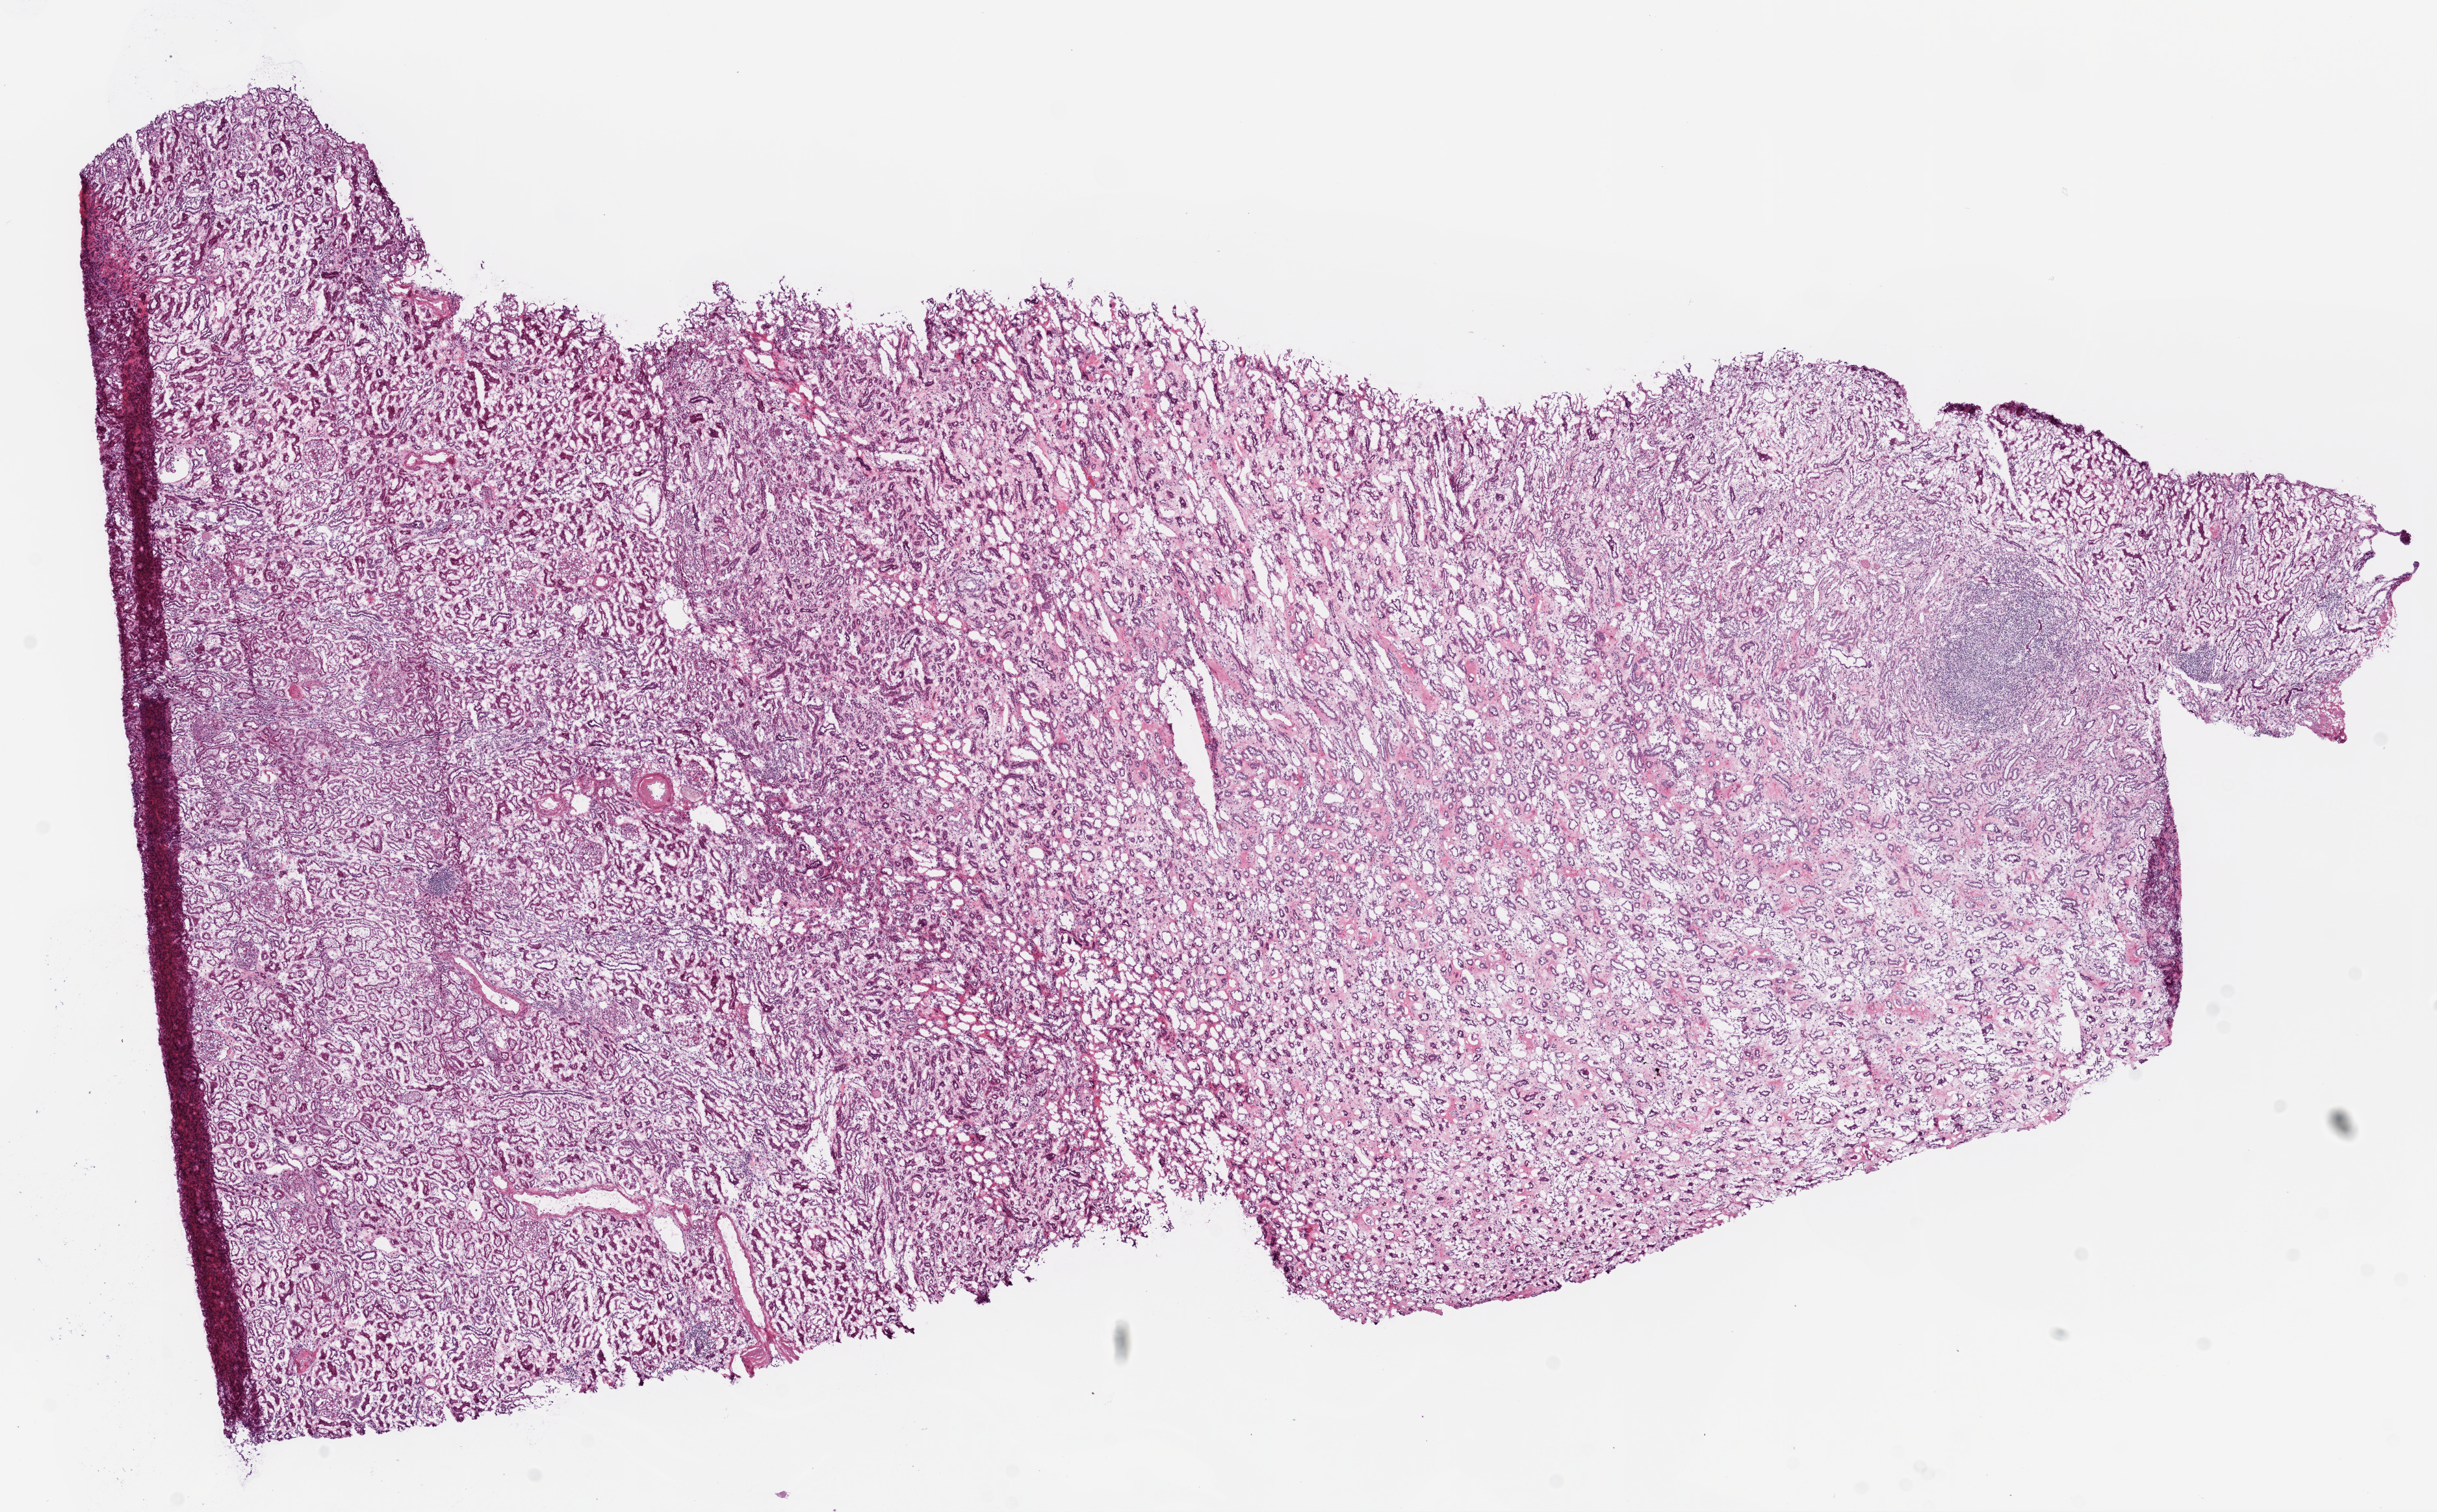
H&E-stained whole-slide image — a low-resolution overview of the entire scanned area, about 15.0 x 9.3 mm (slide scanned at 20x), frozen section, kidney, solid tissue normal (non-tumour tissue) sample. Female patient; age at initial diagnosis 82 years.
* this section: solid tissue normal sample (biorepository sample class)
* patient diagnosis: Clear cell adenocarcinoma, NOS